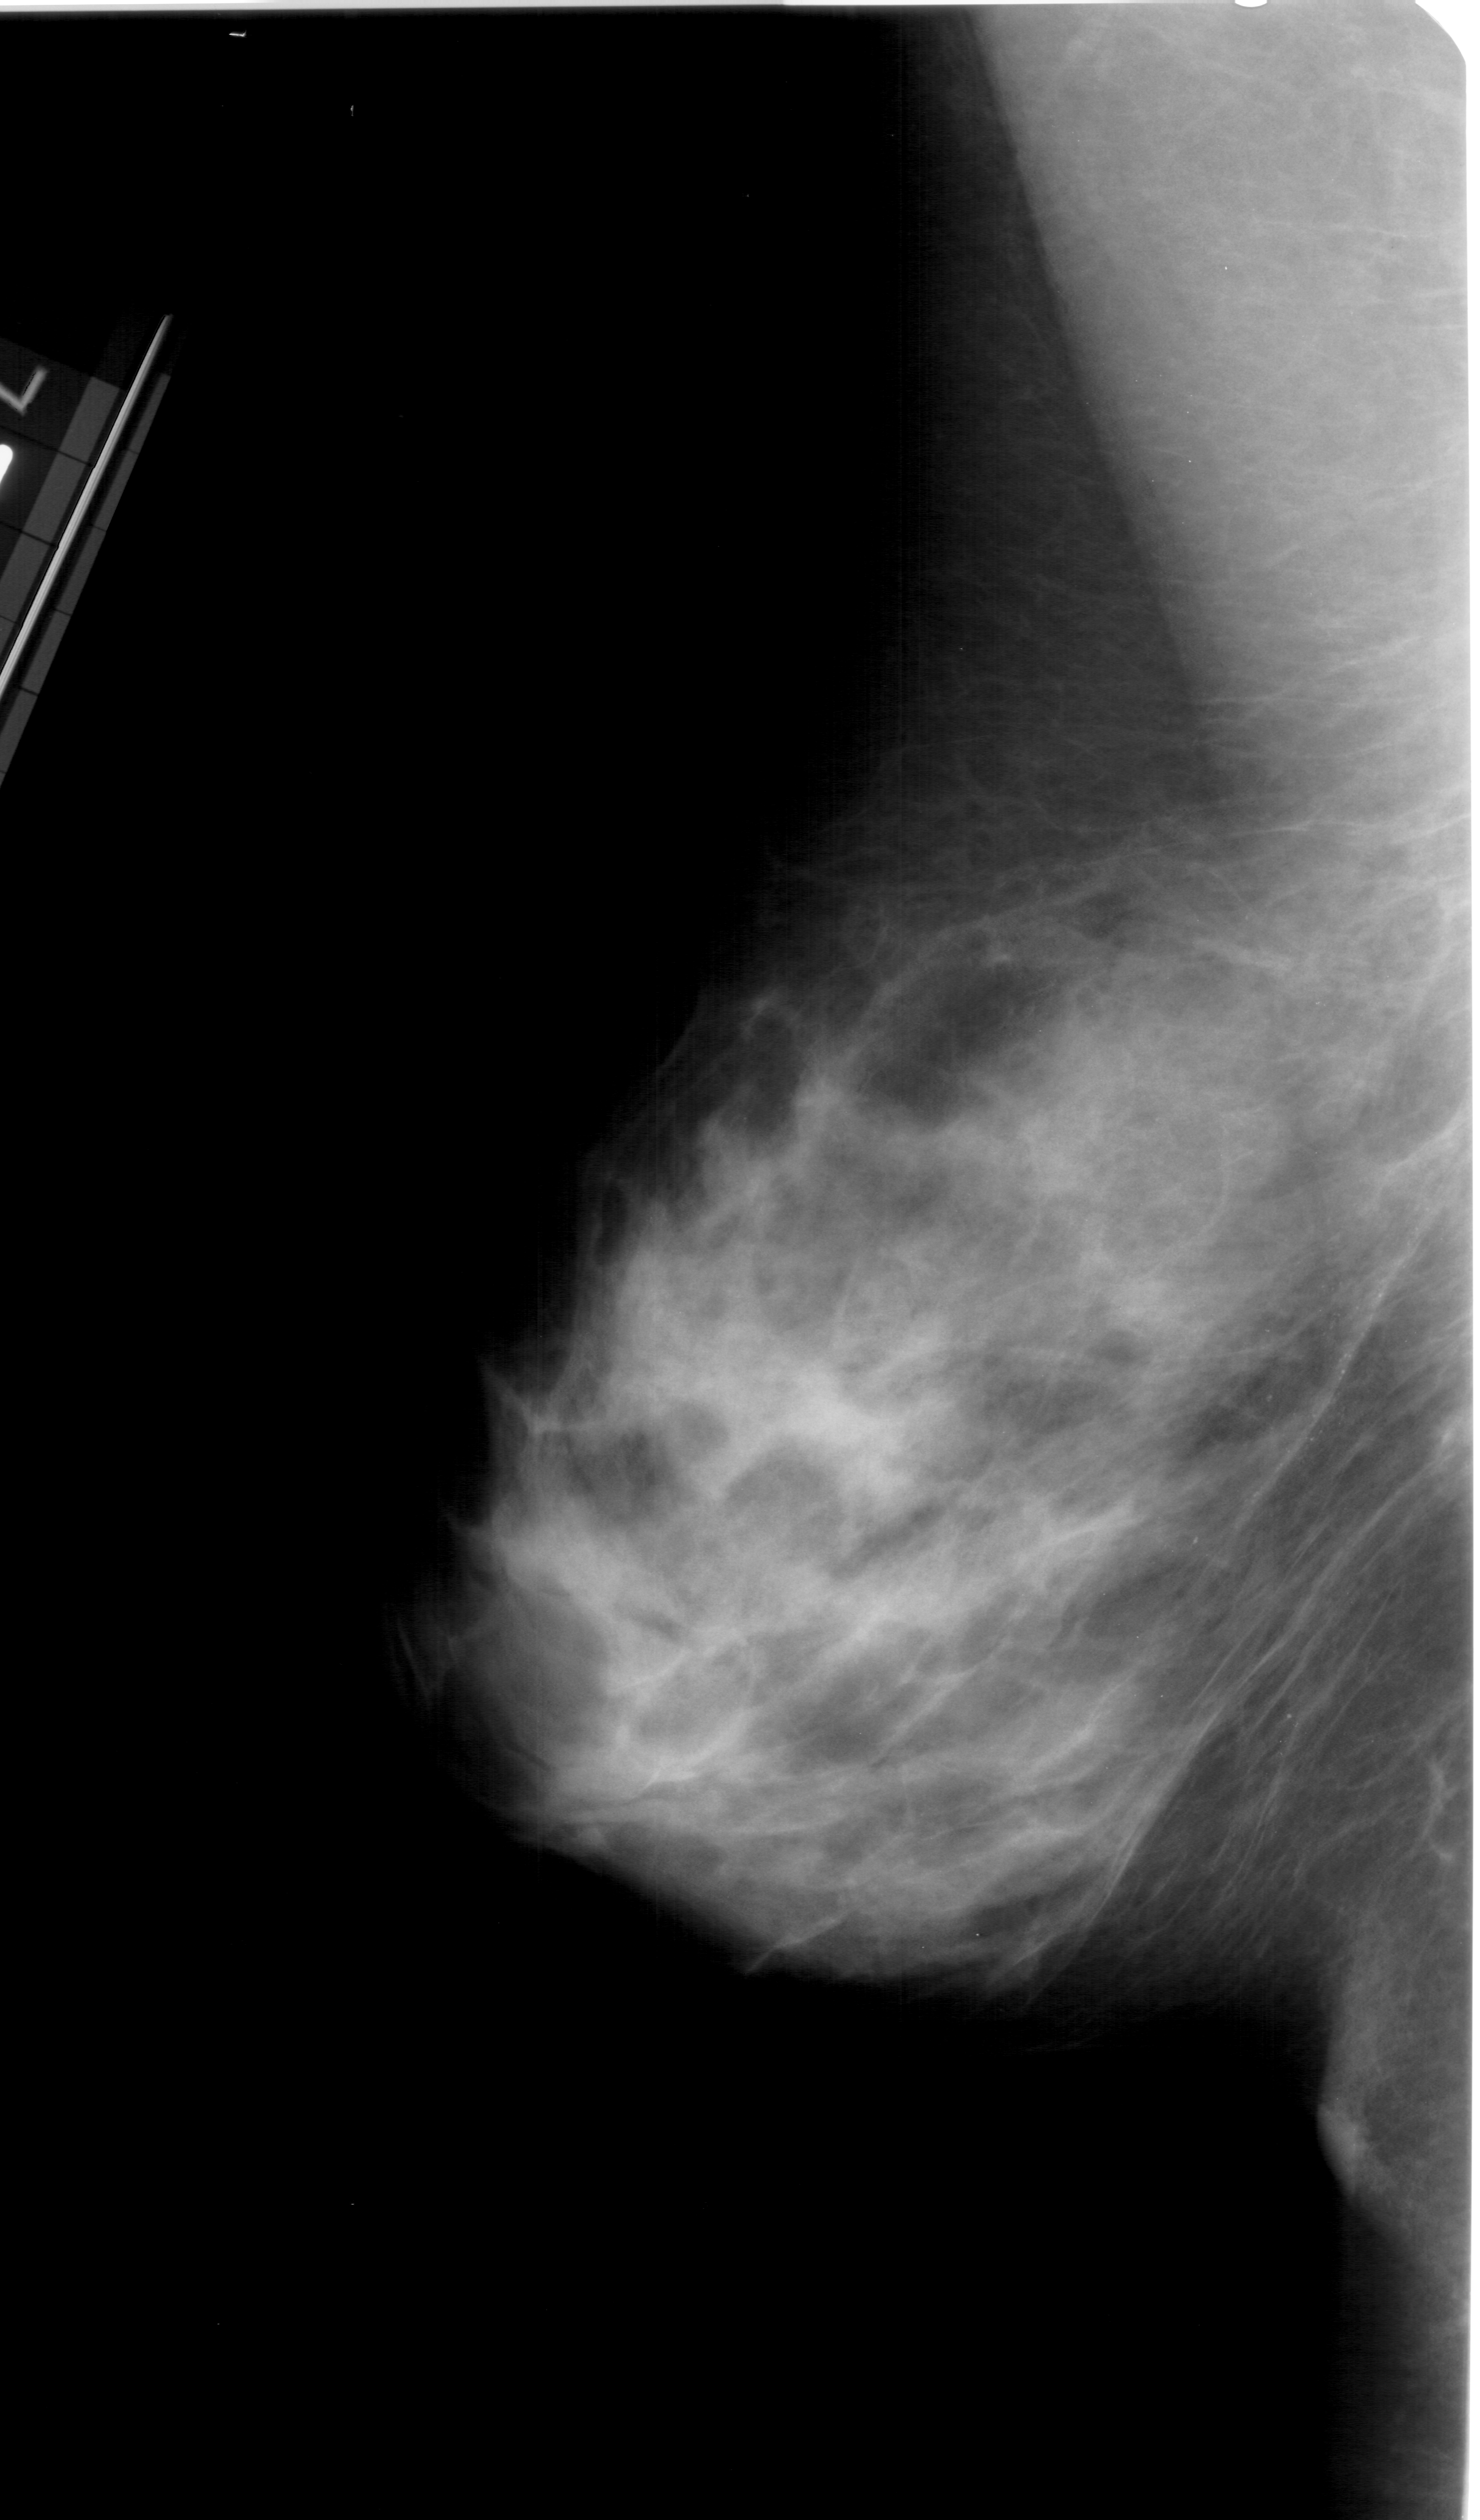
Scanned film-screen mammogram; left breast; mediolateral oblique (MLO) view; BI-RADS breast density category 4 (scale 1–4).
- Abnormality record for this image: calcifications, morphology pleomorphic, distribution segmental; BI-RADS assessment category 4; subtlety rating 4 on a 1 (subtle) to 5 (obvious) scale; pathology result (as recorded, not read from the image): benign.